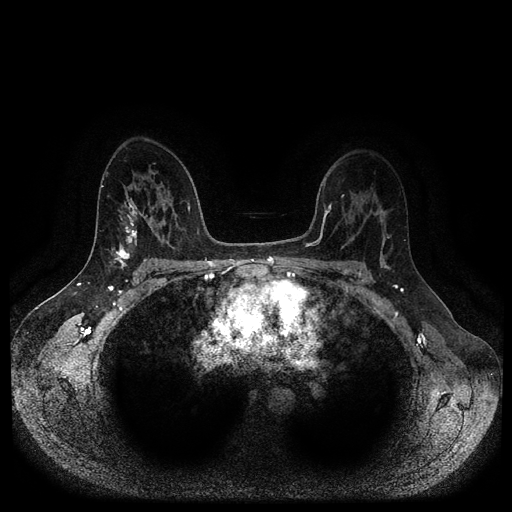
Breast MRI (dynamic contrast-enhanced, multi-phase), one axial slice; slice 65 of 116 in the series (ordered by position); dynamic contrast-enhanced series, time point 2 of 5 at this slice position (early post-contrast); 1.5 T; TE 2.6 ms, TR 5.3 ms; 2 mm slice thickness; 512 × 512 image matrix, field of view 360 × 360 mm. Female patient, age 45 years.
Outlined on this slice (semi-automatic segmentation, software-assisted and operator-edited):
- breast lesion (labelled benign in the annotation): bounding box [x1, y1, x2, y2] px = [118, 210, 138, 246]
- breast lesion (labelled 'tumour' in the annotation; benign lesions carry a separate 'benign' label): [112, 246, 132, 270]